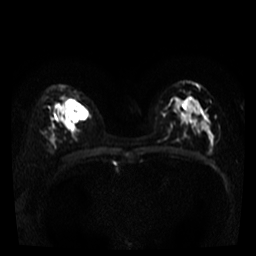
Breast MRI, one axial slice; position 25 of 40 along the scan axis; diffusion-weighted series; image 2 of 4 stored at this slice position (different b-values; order by instance number); 3 T; 5 mm slice thickness; 256 × 256 image matrix, field of view 280 × 280 mm. Female patient.
Structures marked on this image (expert manual segmentation):
- tumour on diffusion-weighted imaging: bounding box (x1, y1, x2, y2) in pixels: (66, 100, 87, 122)